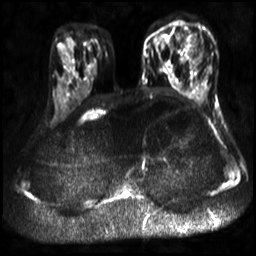
Breast MRI, one axial slice. Position 15 of 30 along the scan axis. Diffusion-weighted series; image 2 of 4 stored at this slice position (different b-values; order by instance number). 3 T. 4 mm slice thickness. 256 × 256 image matrix, field of view 320 × 320 mm. Female patient.
Annotated regions visible in this slice (outlined manually by an expert reader):
- tumour on diffusion-weighted imaging: bounding box (x1, y1, x2, y2) in pixels: (184, 30, 201, 56)